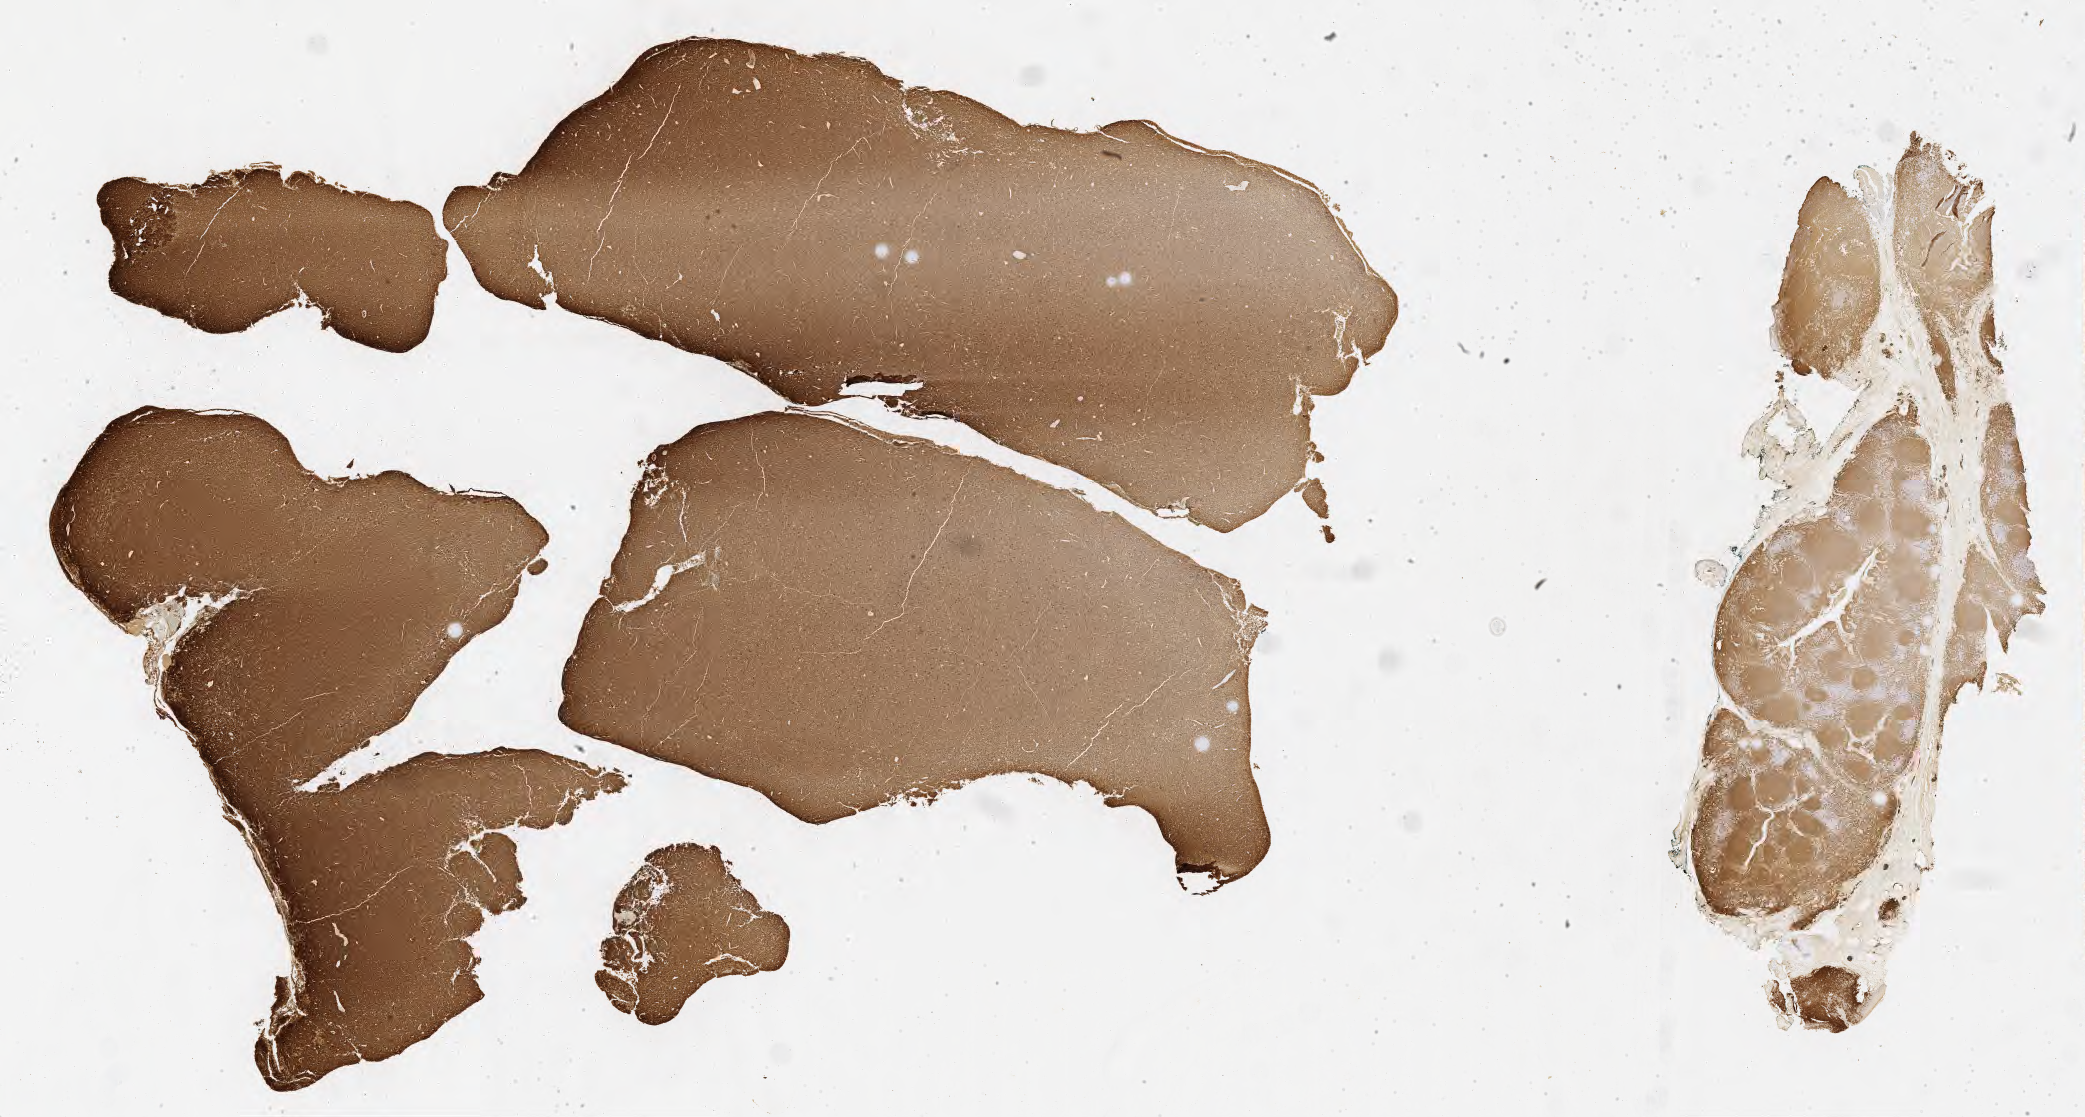
IHC for CD20, whole-slide image — shown as a low-resolution overview of the whole scanned area (about 33.7 x 18.1 mm). Specimen: tumor tissue. Anatomic site: peritoneum. Female, age 7 years at initial diagnosis.
- diagnosis: Burkitt lymphoma, NOS